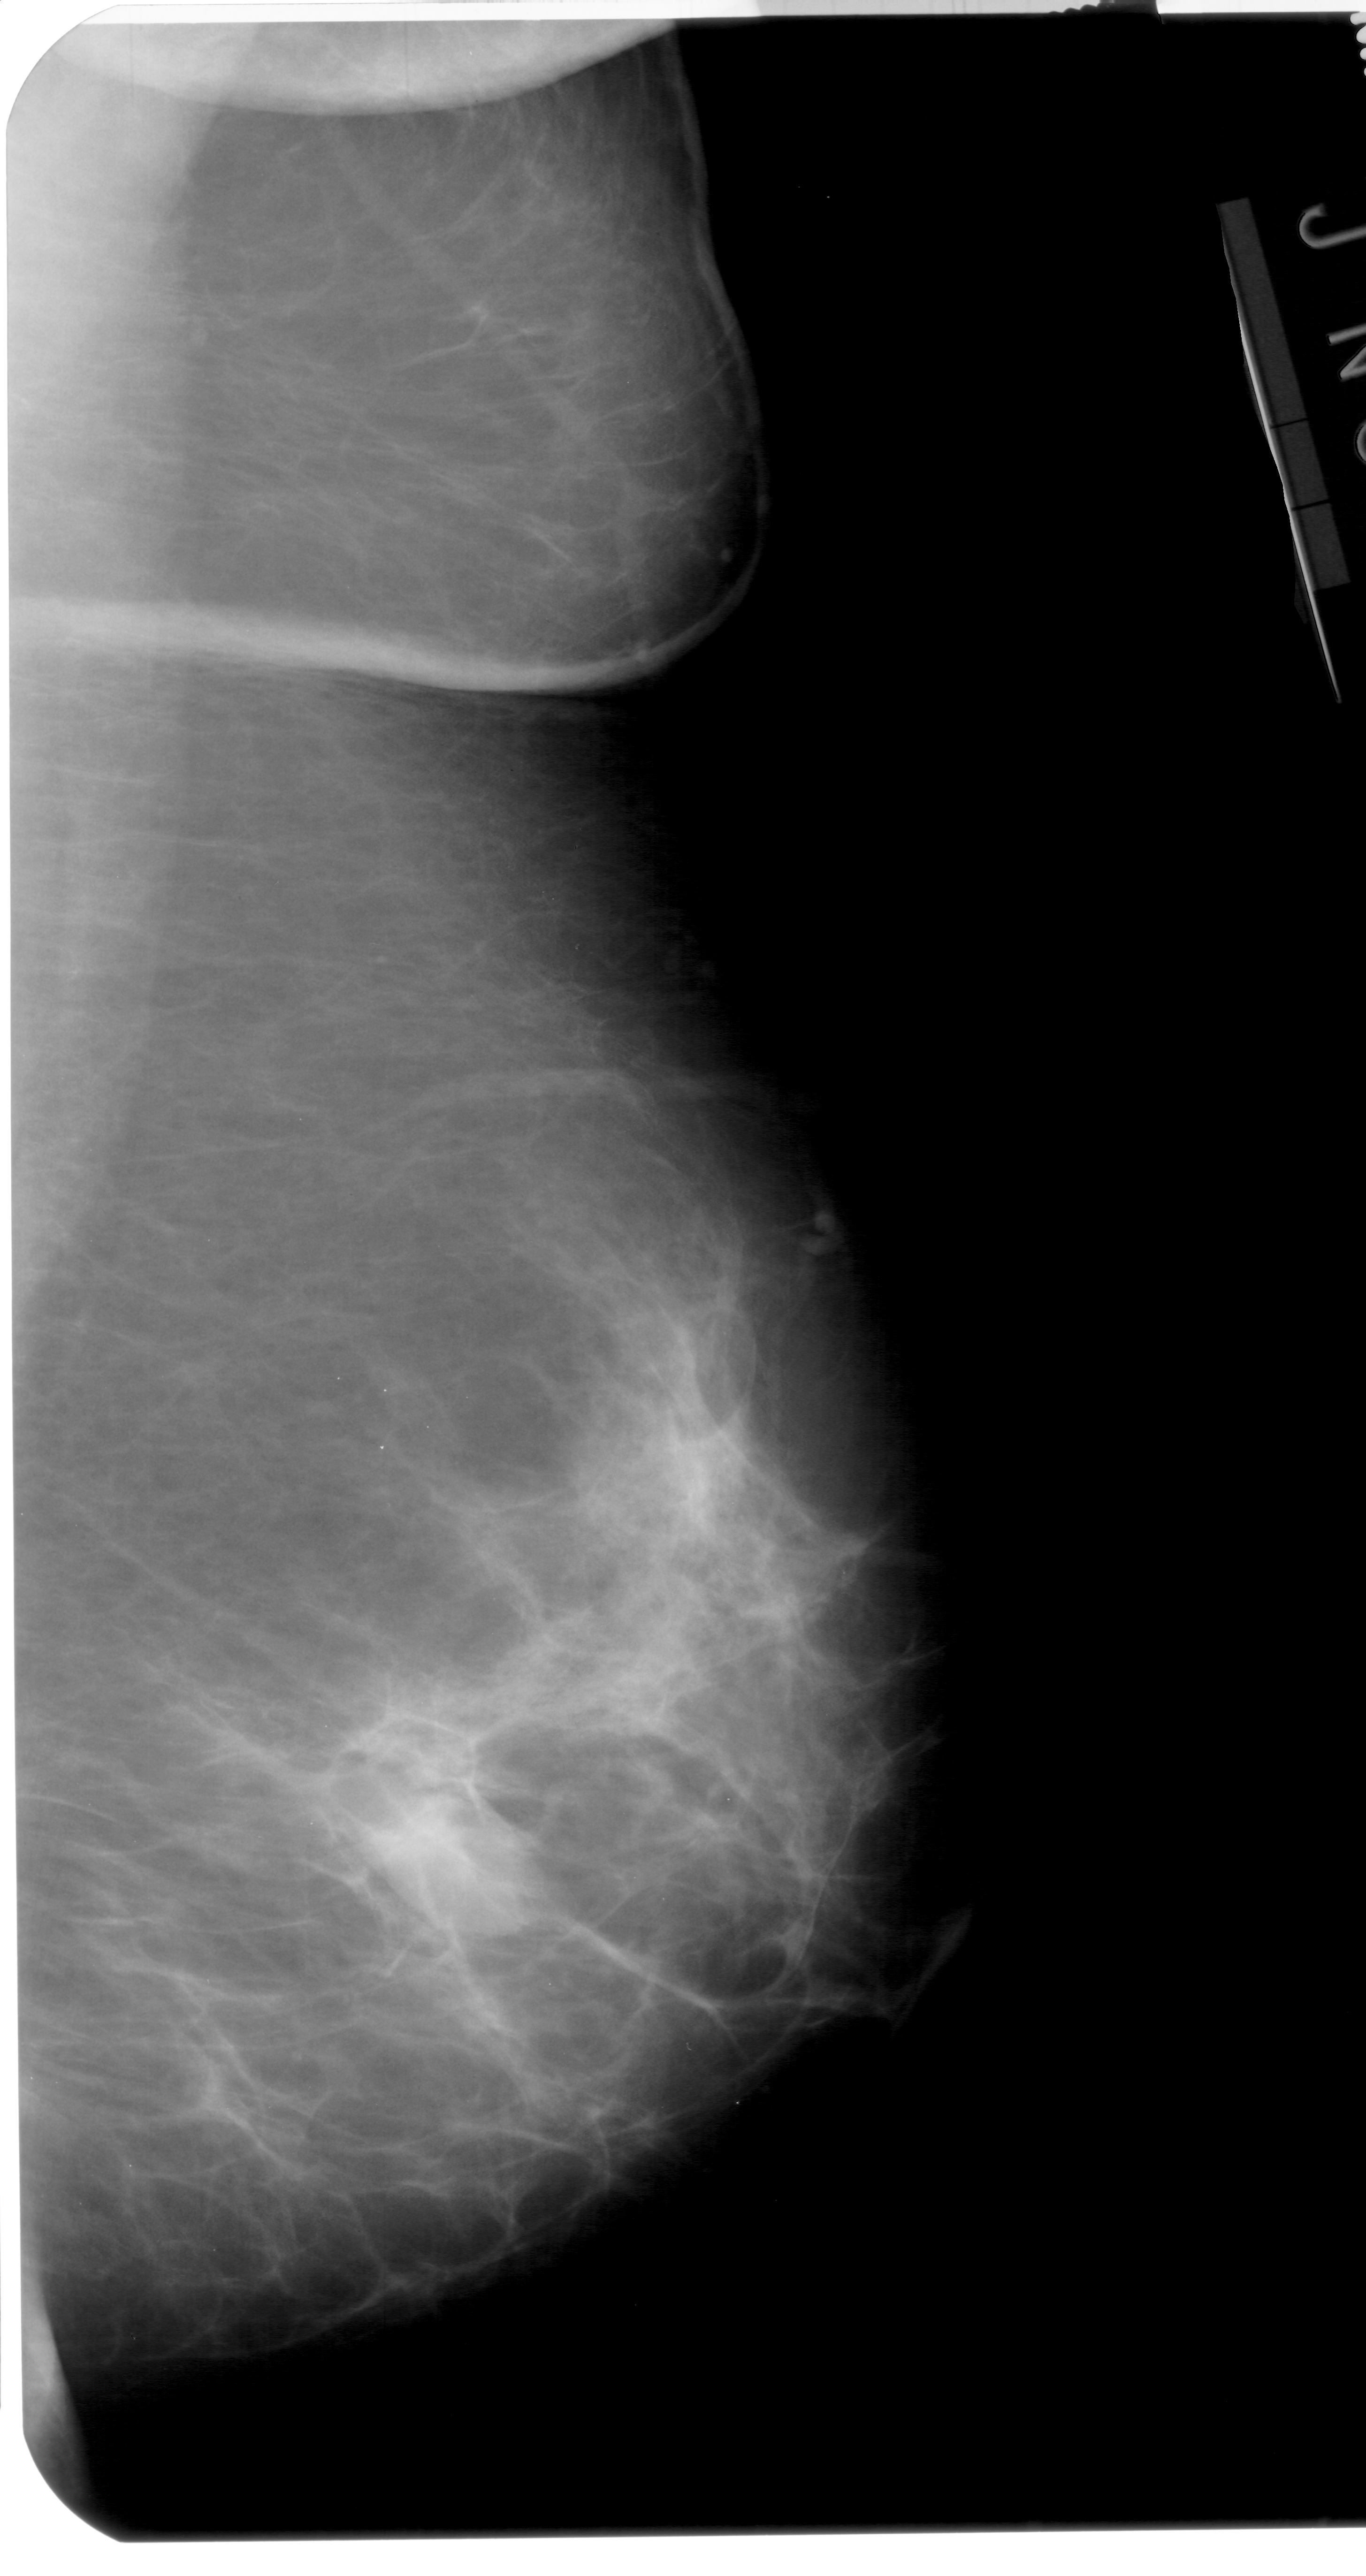
Digitized screen-film mammogram; right breast; MLO view; BI-RADS breast density category 3 (scale 1–4).
Abnormality record for this image: mass, shape oval, margins circumscribed; BI-RADS assessment category 4; subtlety rating 5 on a 1 (subtle) to 5 (obvious) scale; pathology (as recorded): benign.